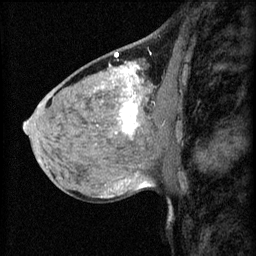
Breast MRI (dynamic contrast-enhanced), one sagittal slice. Position 37 of 60 along the scan axis. 3 images stored at this slice position (order not interpretable as contrast timing). 1.5 T. TE 4.2 ms, TR 8.2 ms. 2.2 mm slice thickness. 256 × 256 image matrix, field of view 180 × 180 mm. Female patient, age 40 years.
Structures marked on this image (semi-automatic segmentation, software-assisted and operator-edited):
- analysis volume of interest (the breast-tissue region the enhancement analysis was run in; not a lesion): bounding box <108,82,175,139> (left, top, right, bottom; pixels)
- tumour enhancement mask (voxels above the 70 % enhancement threshold inside the analysis volume of interest): <116,82,141,137>